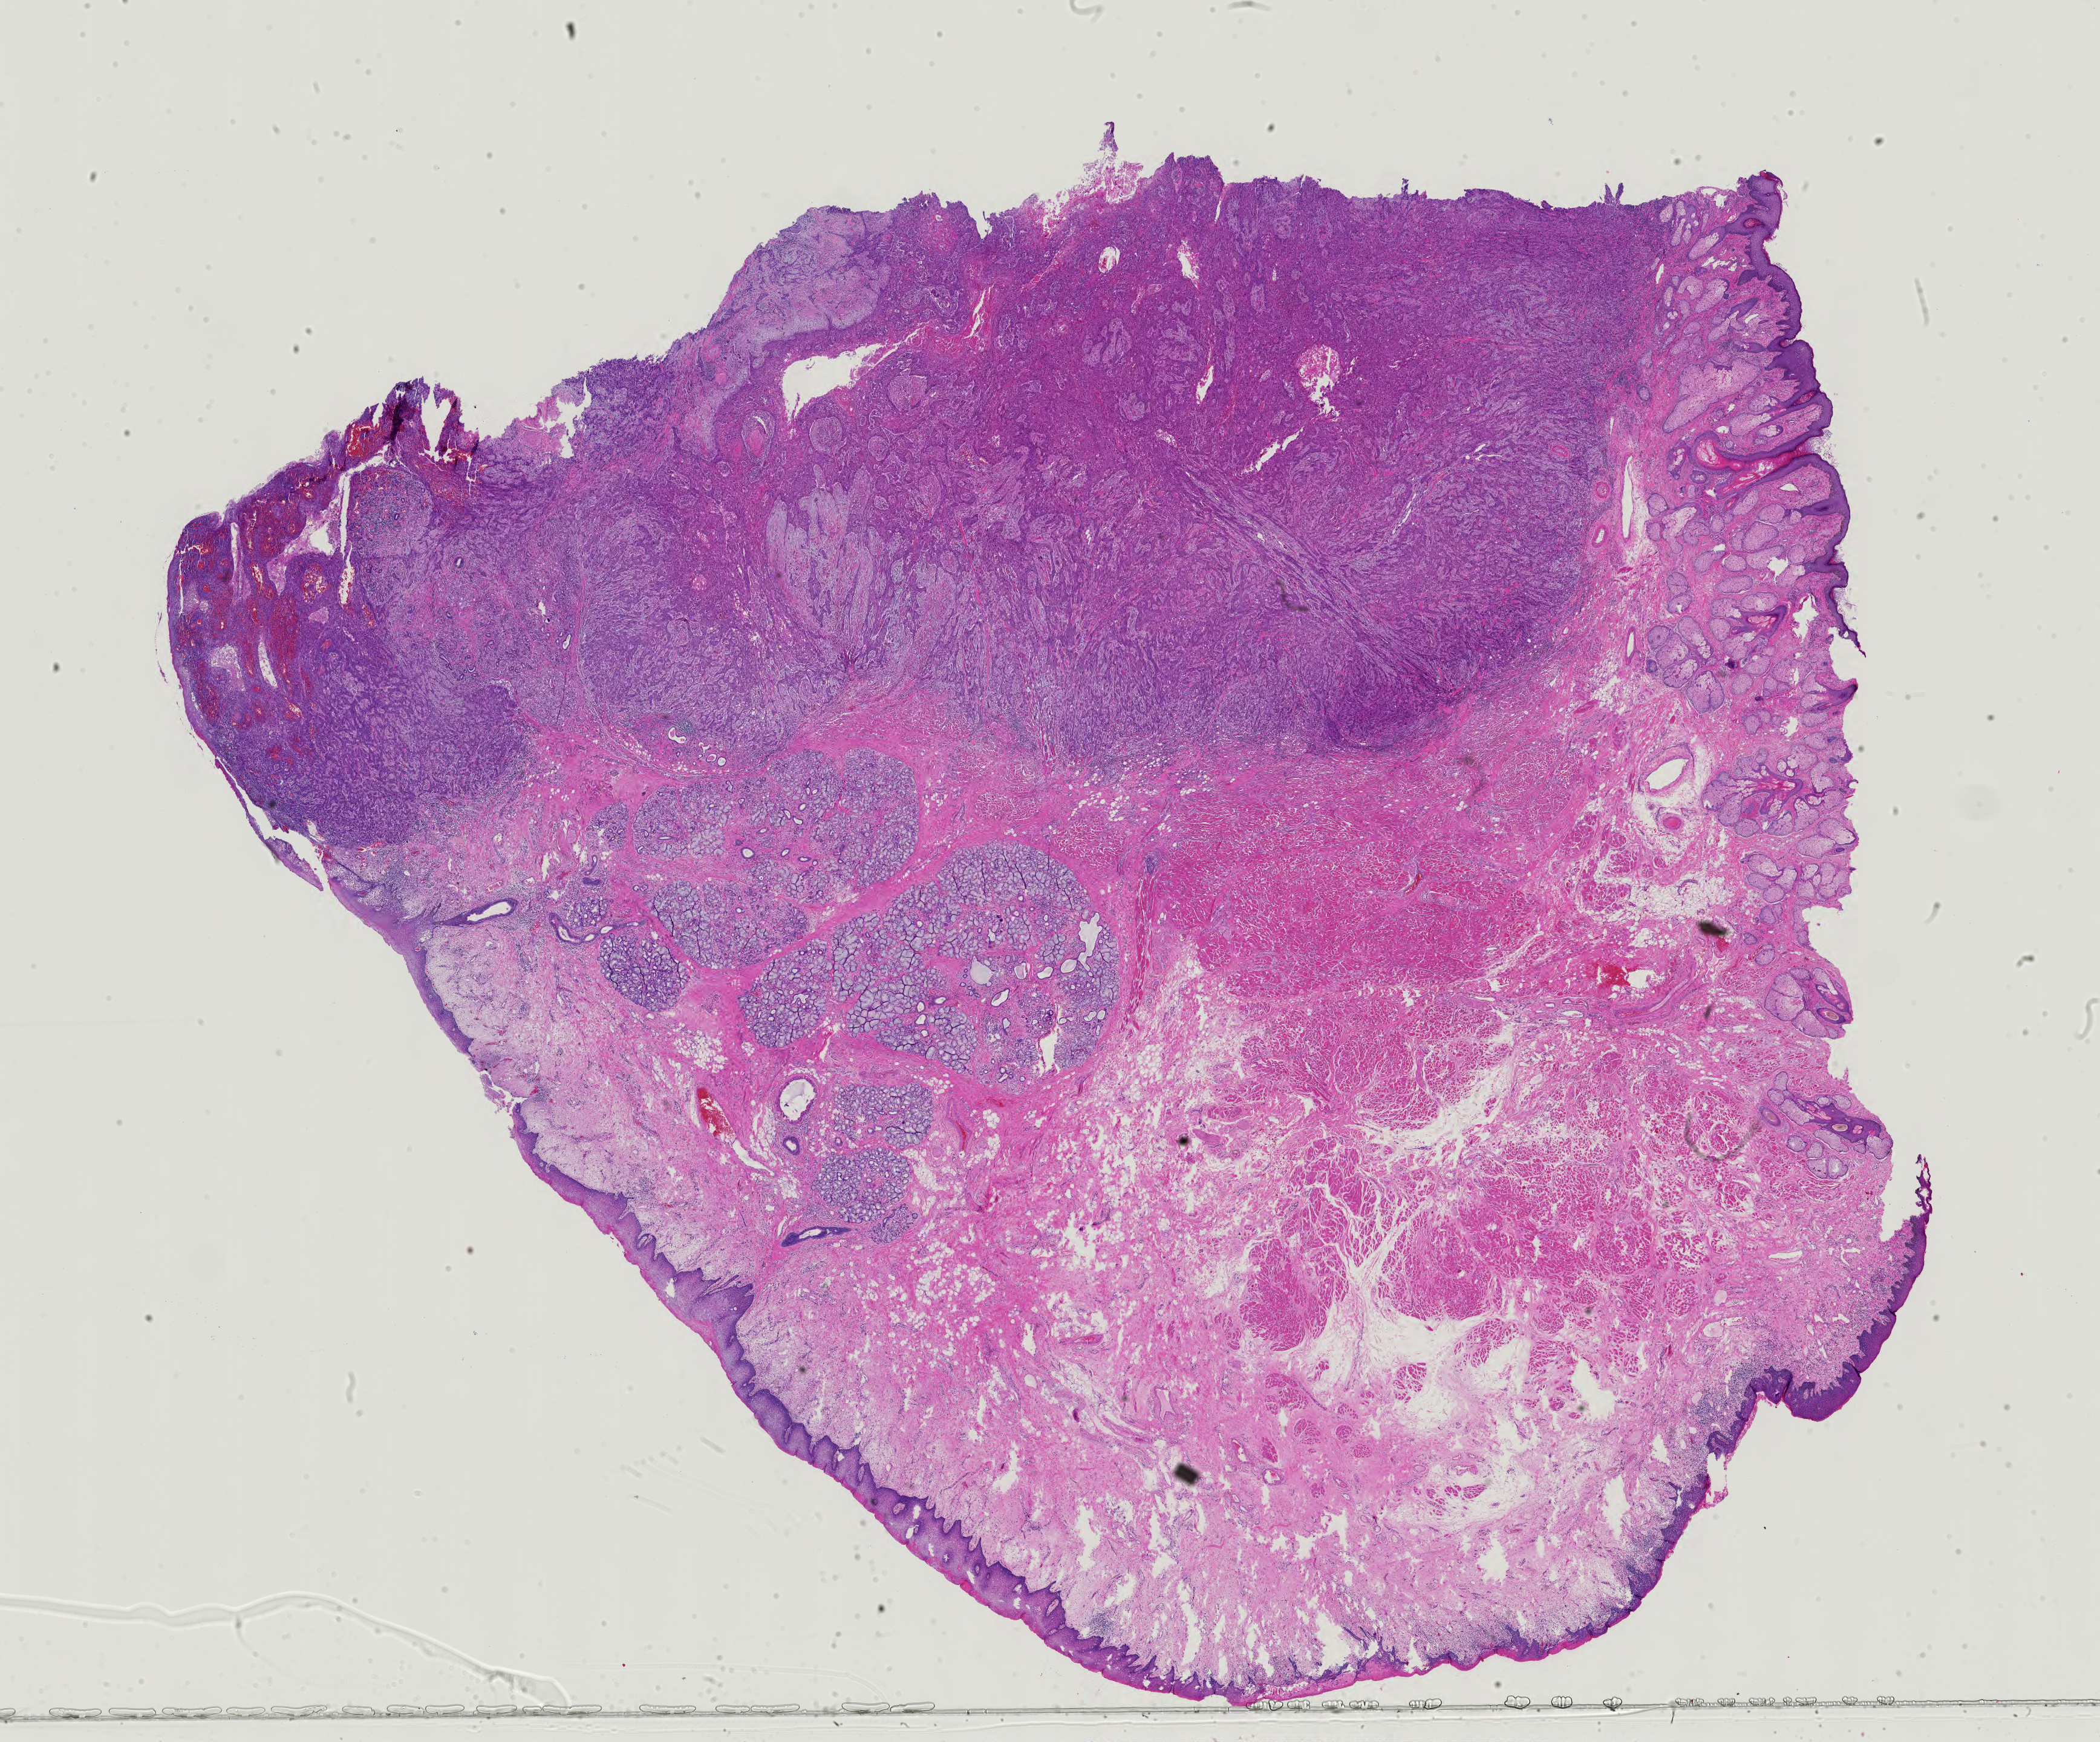
Digitized Hematoxylin and eosin (H&E) stained tissue section (whole slide), a low-resolution overview of the entire scanned area, about 25.2 x 20.9 mm. Formalin-fixed paraffin-embedded (FFPE) diagnostic section. Head and neck, primary tumour sample. Male patient; age at initial diagnosis 56 years. Histologic grade: G2 (moderately differentiated).
• AJCC pathologic stage: IVA (7th edition)
• pathologic diagnosis: Squamous cell carcinoma, NOS (floor of mouth, NOS)
• lymph nodes positive (case pathology): 2 of 82 examined
• TNM: T4a N2b M0
• laterality: right